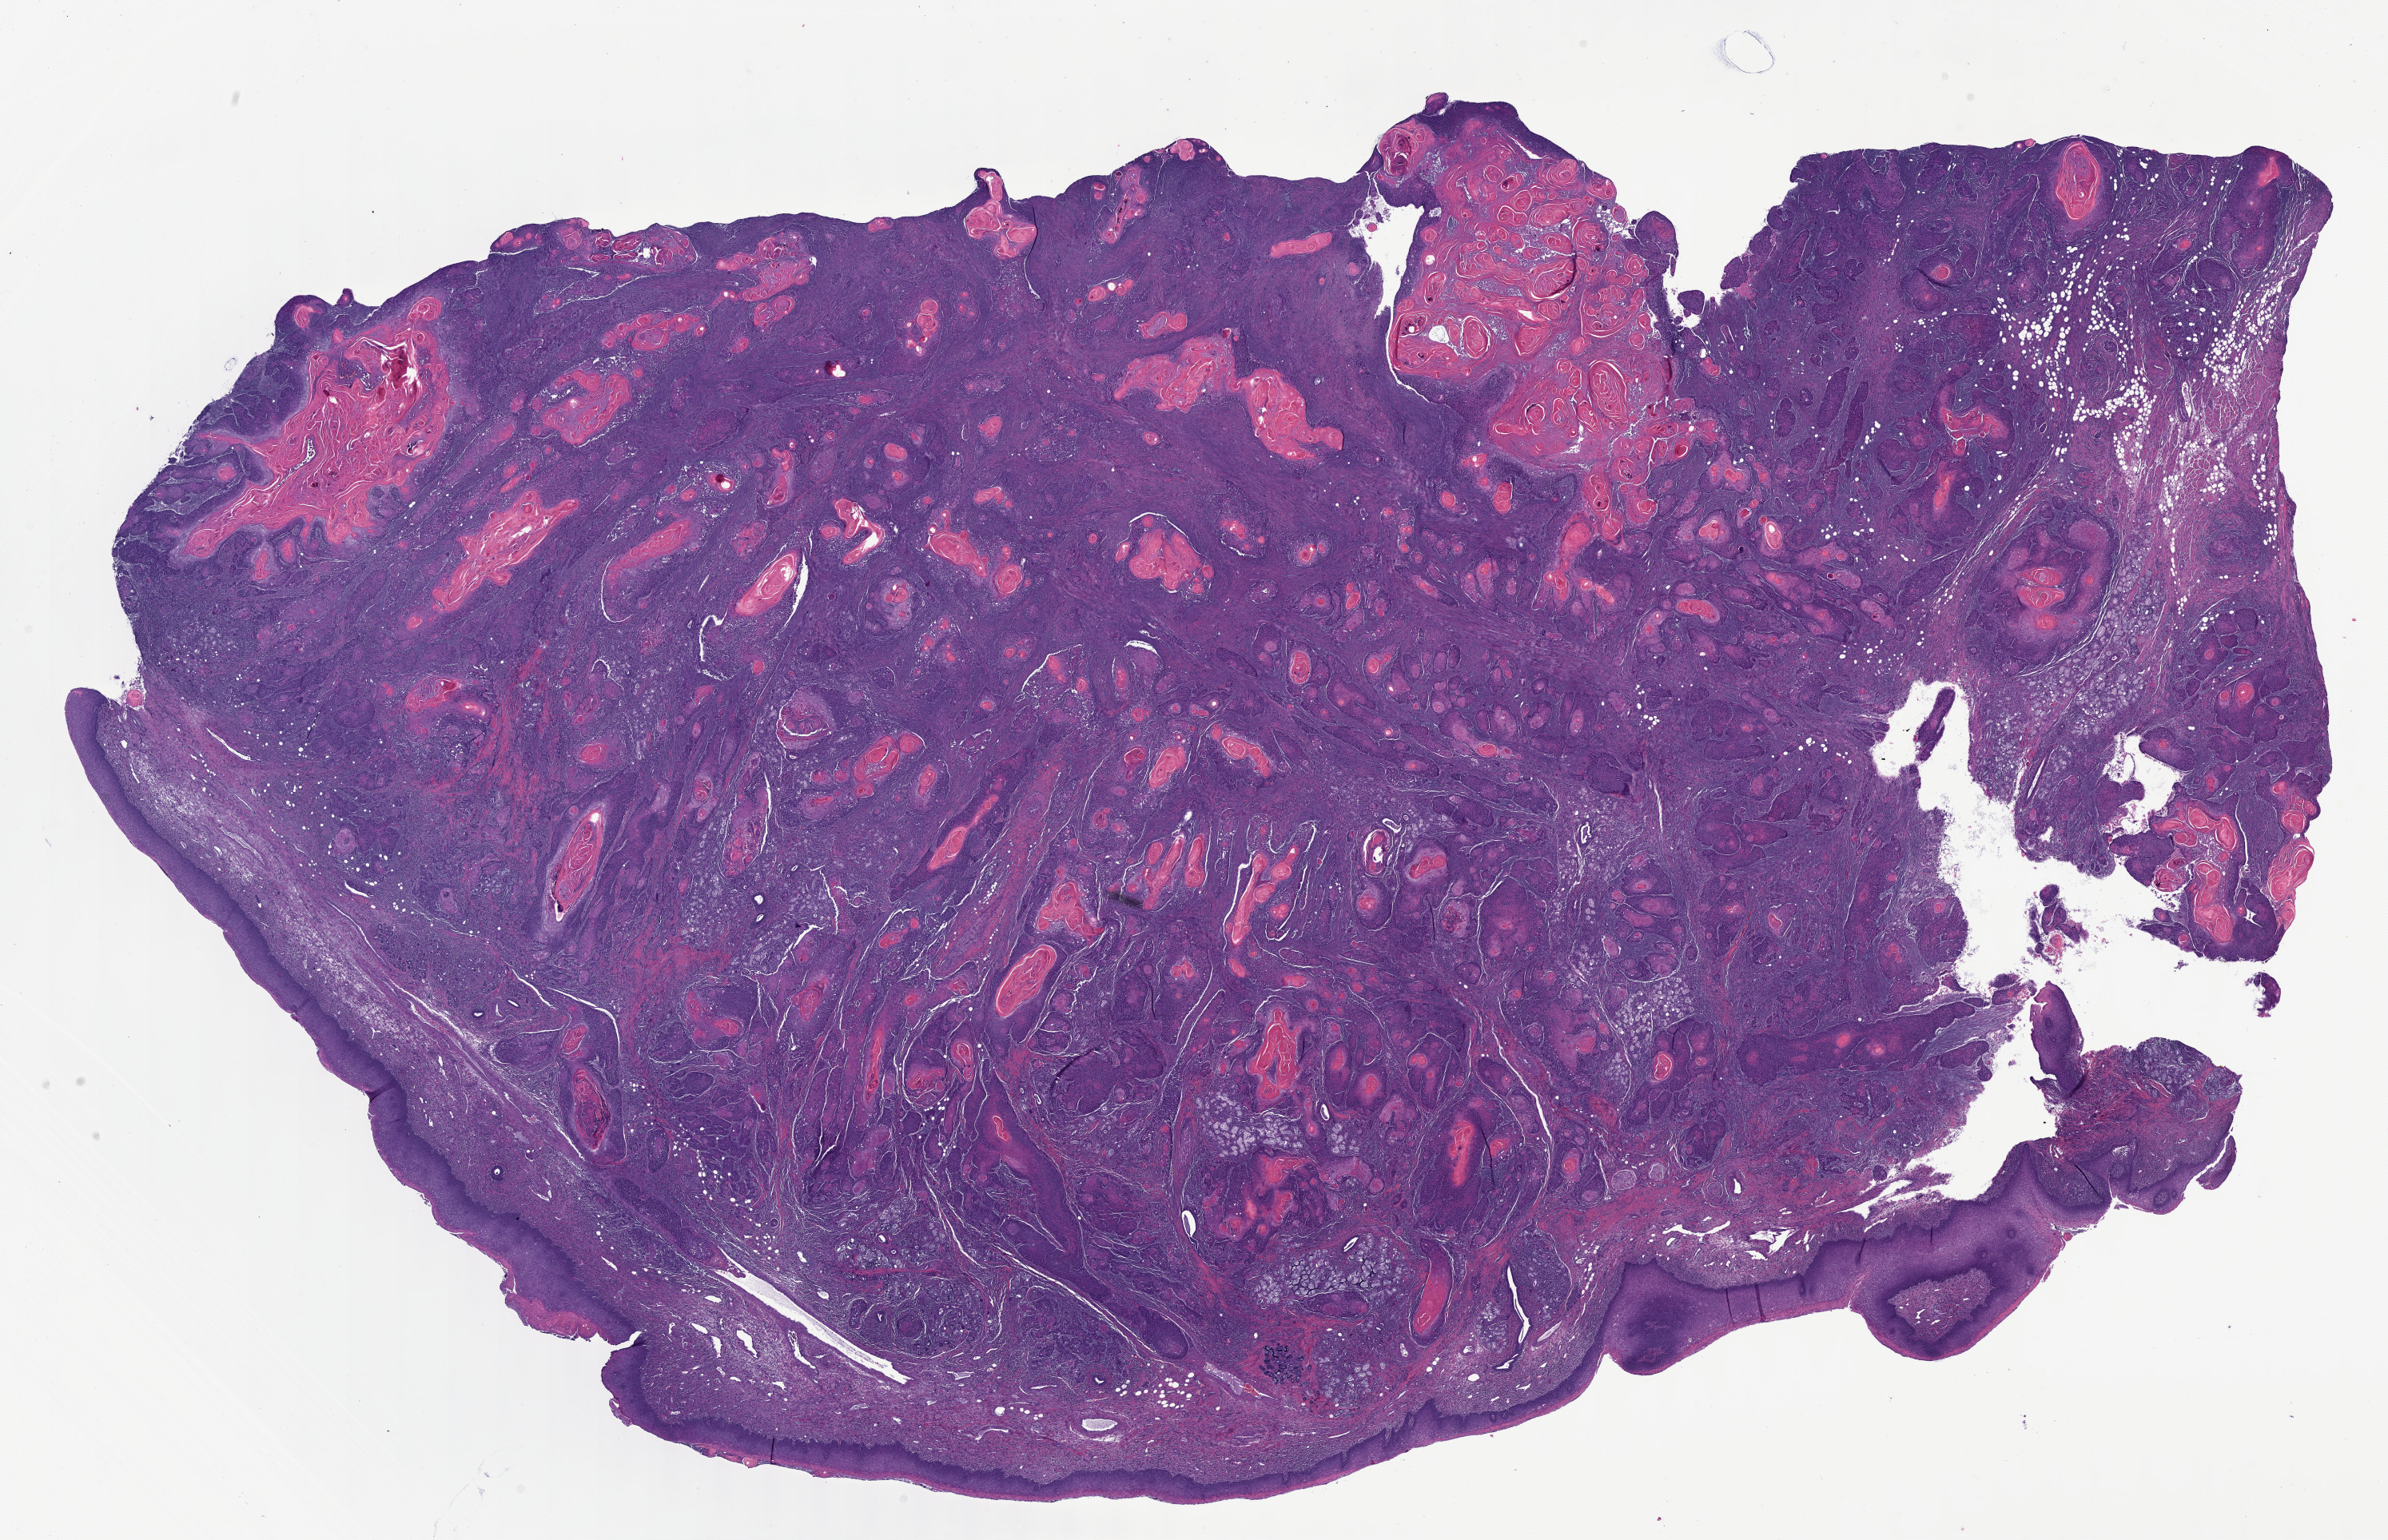
Digitized H&E tissue section (whole slide) — low-resolution overview of the scanned area, about 24.1 x 15.6 mm (acquisition: 40x scan). Formalin-fixed paraffin-embedded (FFPE) diagnostic section. Sample: primary tumour, head and neck. Male patient; age at initial diagnosis 62 years. Histologic grade: G2 (moderately differentiated).
- AJCC pathologic stage: IVA
- diagnosis: Squamous cell carcinoma, NOS (base of tongue, NOS)